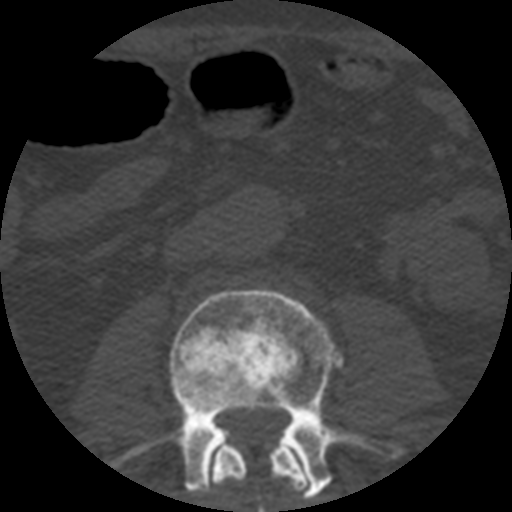
CT including the spine, one axial slice; slice 130 of 508 in the series (ordered by position); reconstruction kernel STANDARD; 120 kVp; bone window (W 1800 / L 400 HU); 1.25 mm slice thickness; 512 × 512 image matrix, field of view 160 × 160 mm. Patient age 57 years. Case-level facts recorded for this patient, not image findings: primary cancer: prostate.
Annotated regions visible in this slice (semi-automatic segmentation, software-assisted and operator-edited):
- L2 vertebra: bounding box <205,433,311,512> (left, top, right, bottom; pixels)
- L3 vertebra: <114,288,404,500>